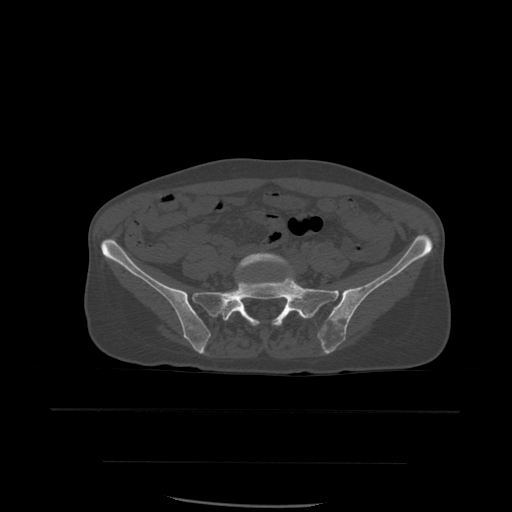
CT including the spine, one axial slice; slice 133 of 574 in the series (ordered by position); bone window (W 1800 / L 400 HU); 512 × 512 image matrix, field of view 392 × 392 mm. Patient age 48 years. Case-level facts recorded for this patient, not image findings: primary cancer: lung; vertebrae with lytic lesions (as recorded): T11.
Outlined on this slice (semi-automatically segmented with operator editing):
- L5 vertebra: bounding box <229,253,303,318> (left, top, right, bottom; pixels)